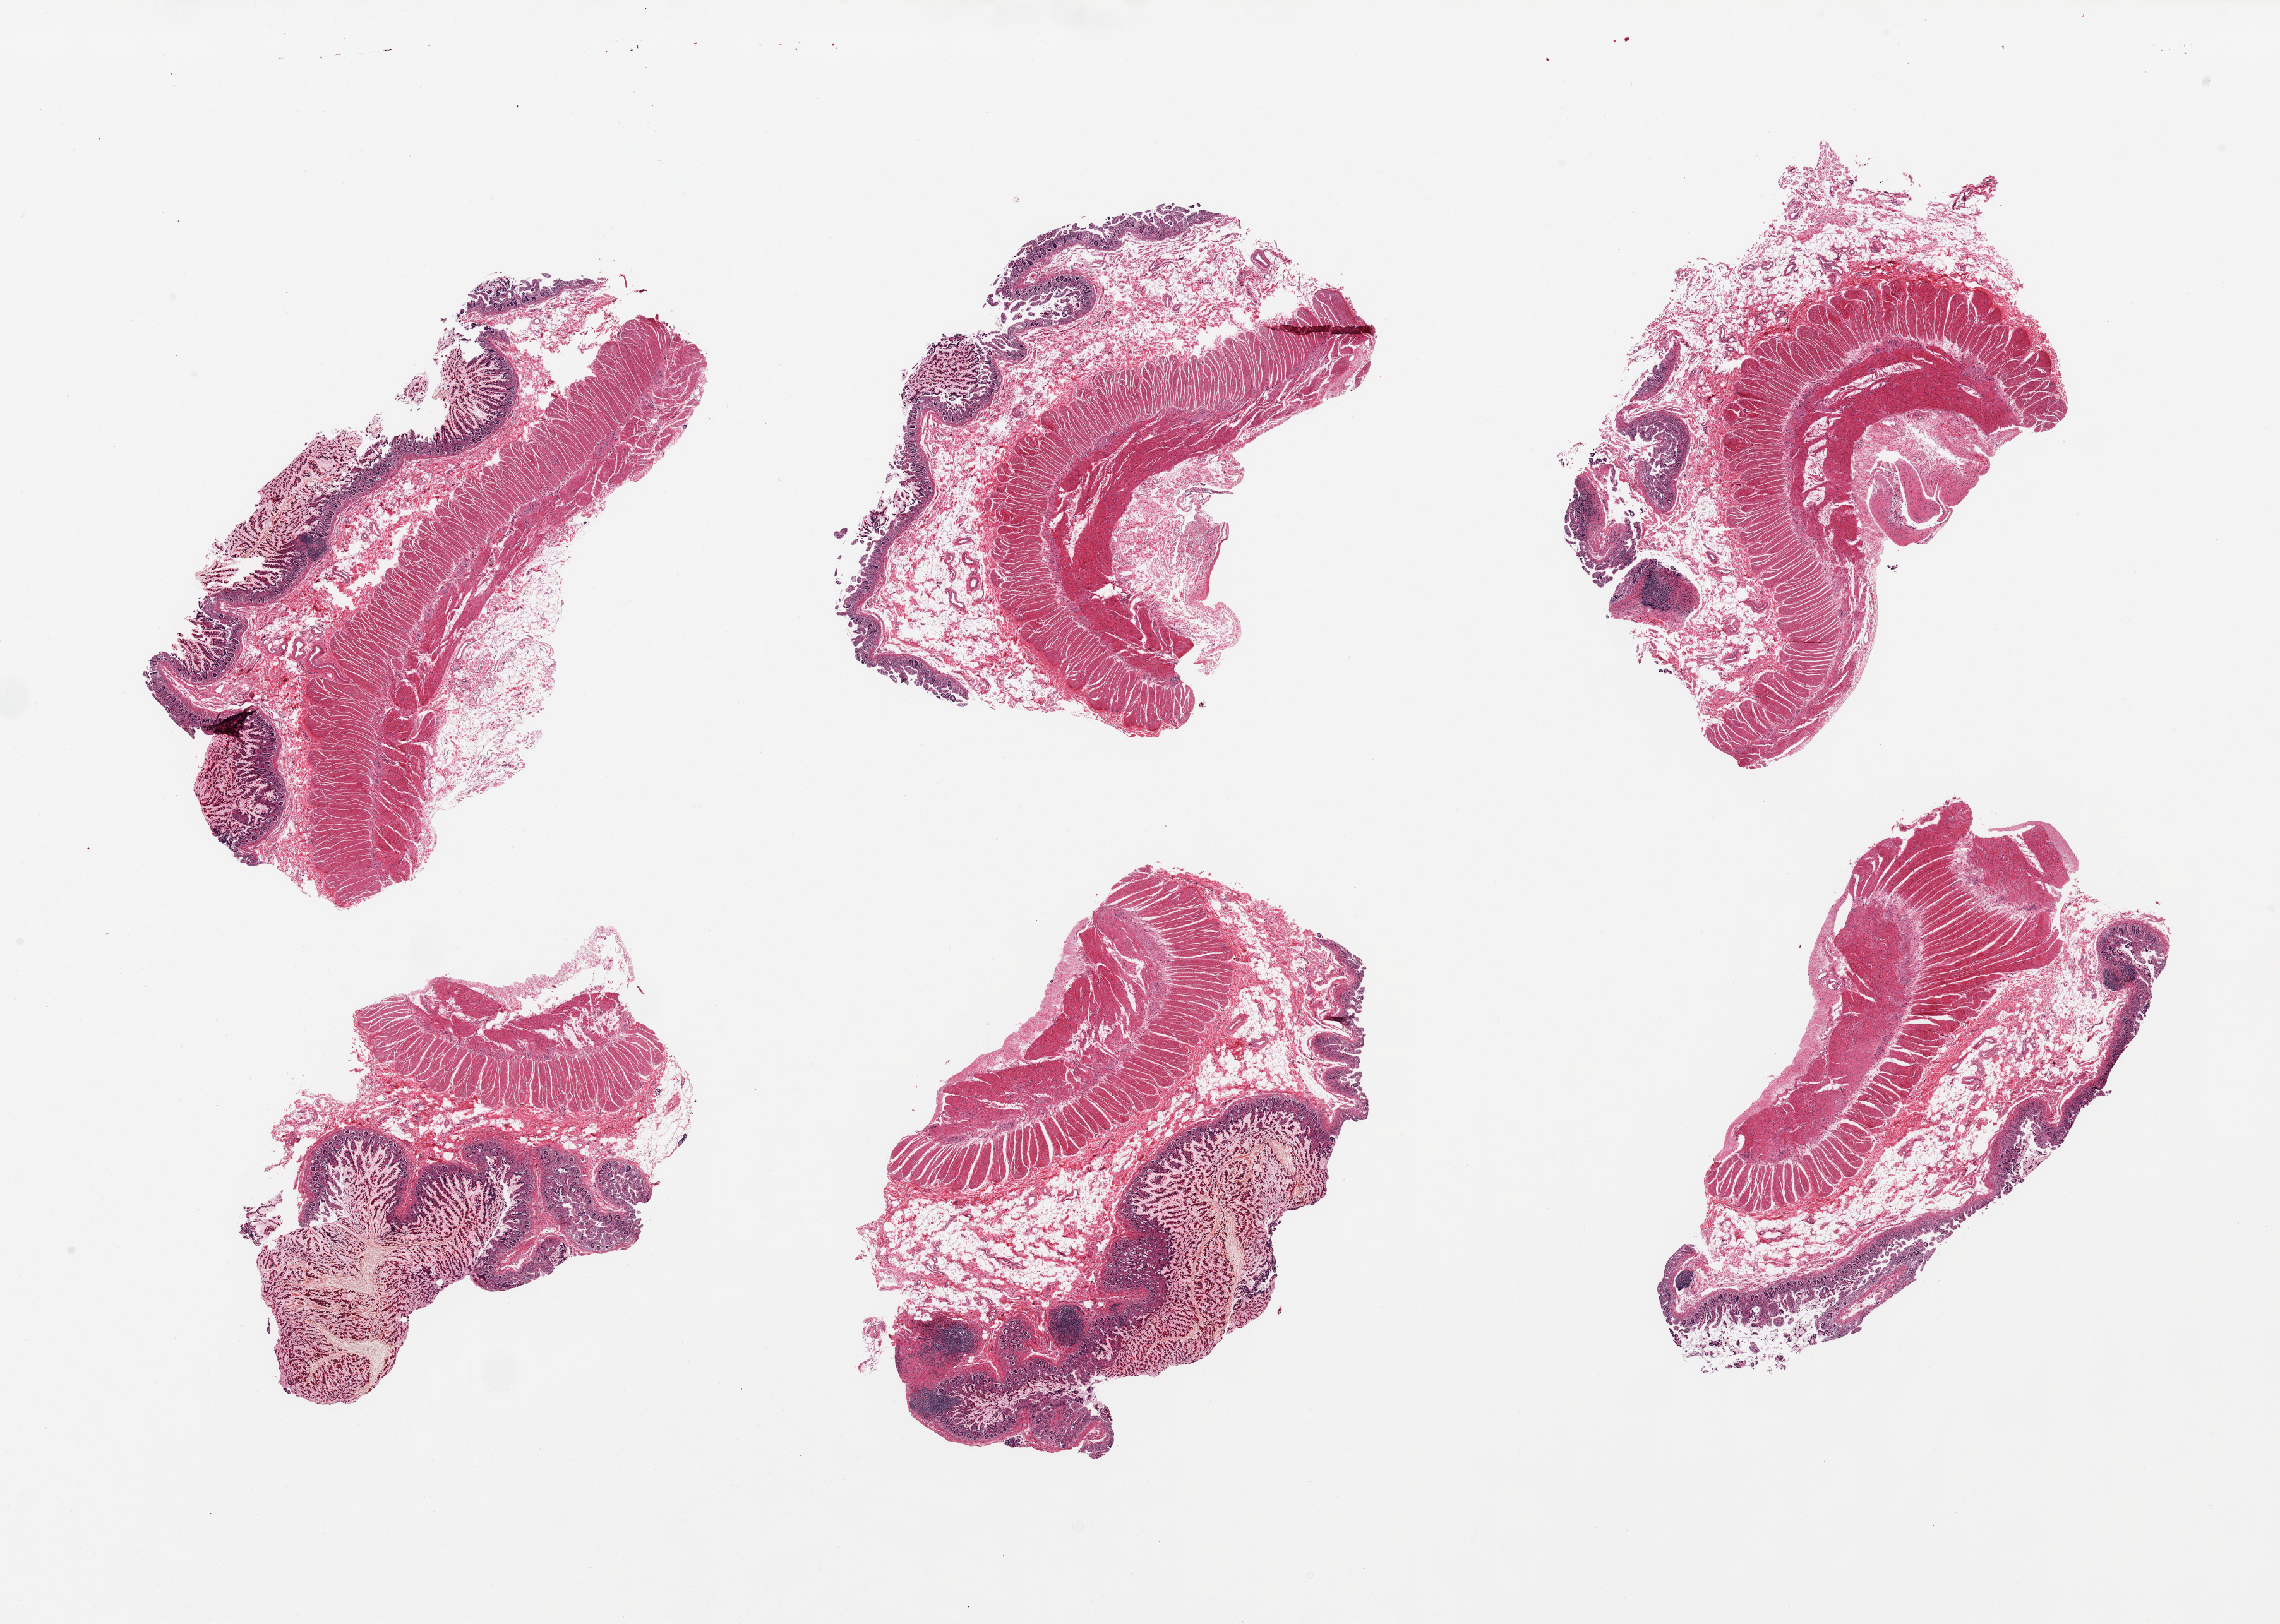
Whole-slide image, H&E stain — whole scanned area (about 28.5 x 20.3 mm, slide scanned at 20x) shown as a low-resolution overview. Donor sex: male.
Specimen: PAXgene-fixed paraffin-embedded (PFPE) section; section of ileum (target tissue); tissue donor sample.